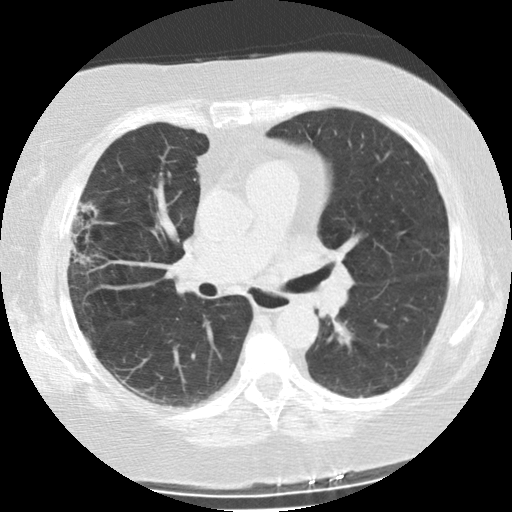
Low-dose screening chest CT, one axial slice. Slice 131 of 225 in the series (ordered by position). Reconstruction kernel STANDARD. 120 kVp. Lung window (W 1500 / L -600 HU). 512 × 512 image matrix.
Outlined on this slice (outlined manually by an expert reader):
- lesion 1 (tumor, upper lobe of right lung): box from (x=71, y=244) to (x=97, y=266) px